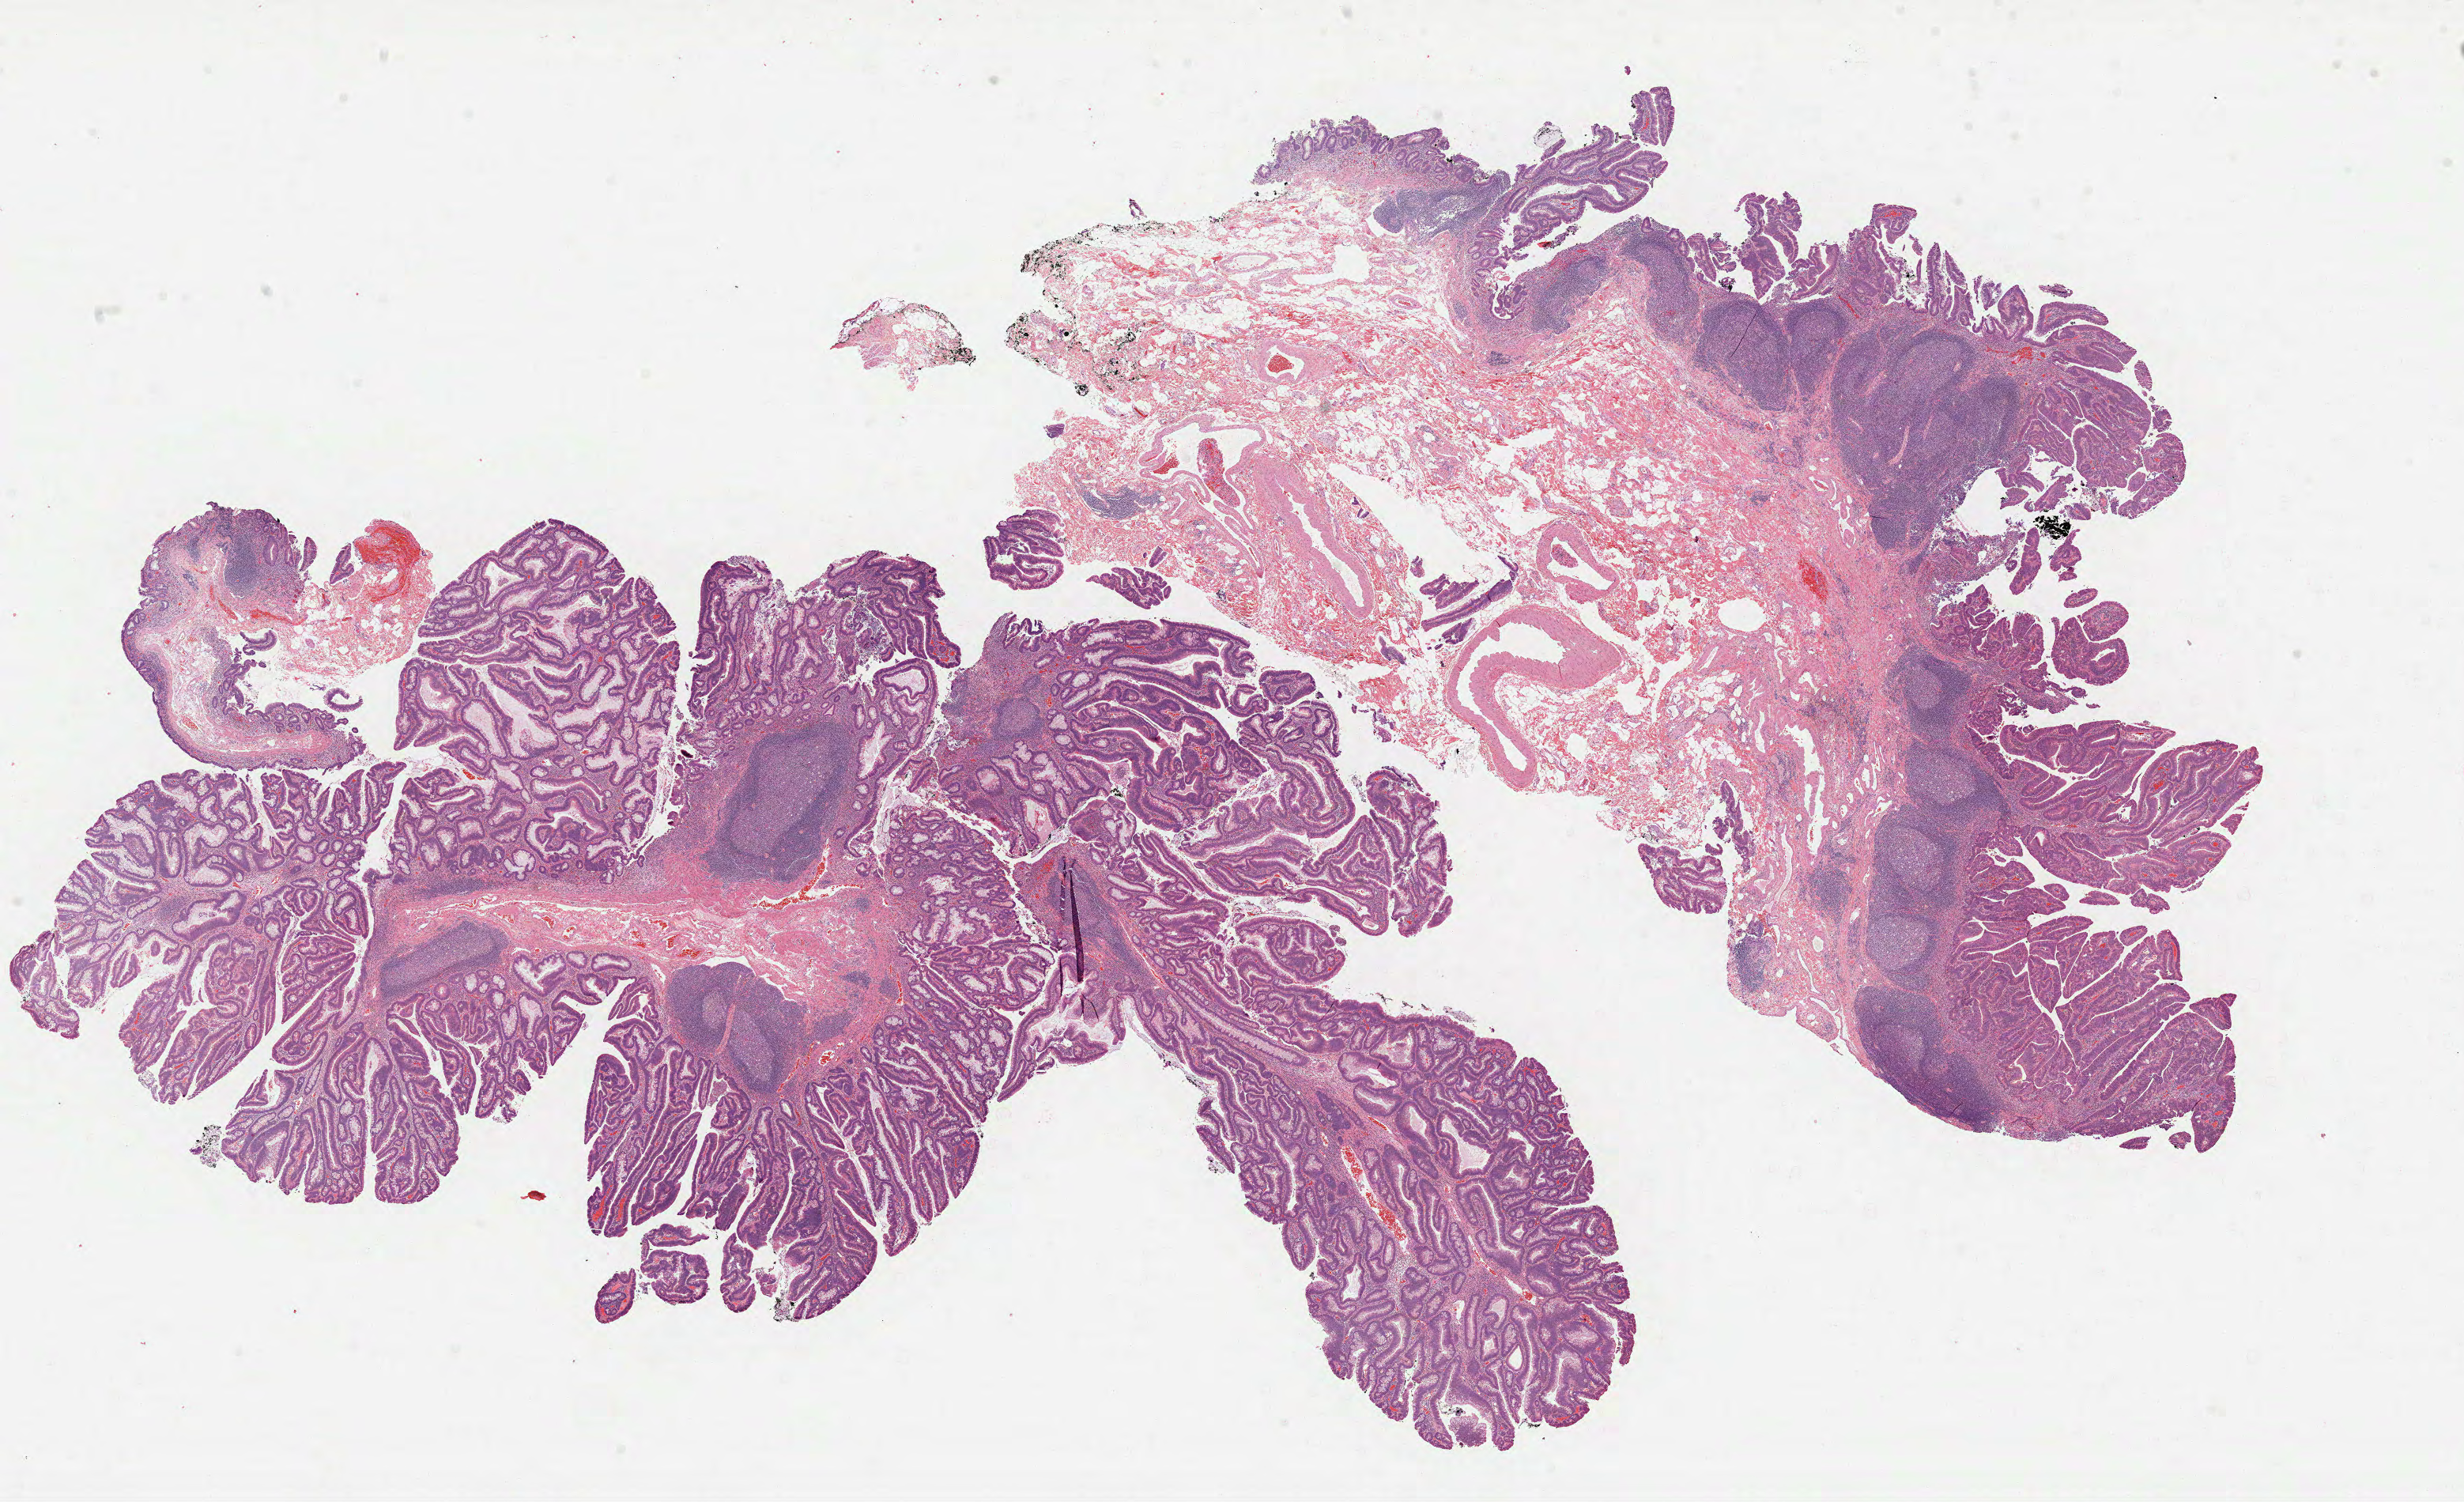
Whole-slide histology image, Hematoxylin and eosin (H&E) stained, a low-resolution overview of the entire scanned area, about 25.1 x 15.3 mm. Formalin-fixed paraffin-embedded (FFPE) diagnostic section. Sample: primary tumour, colon. Male patient; age at initial diagnosis 50 years.
Diagnosis: Adenocarcinoma, NOS (cecum).